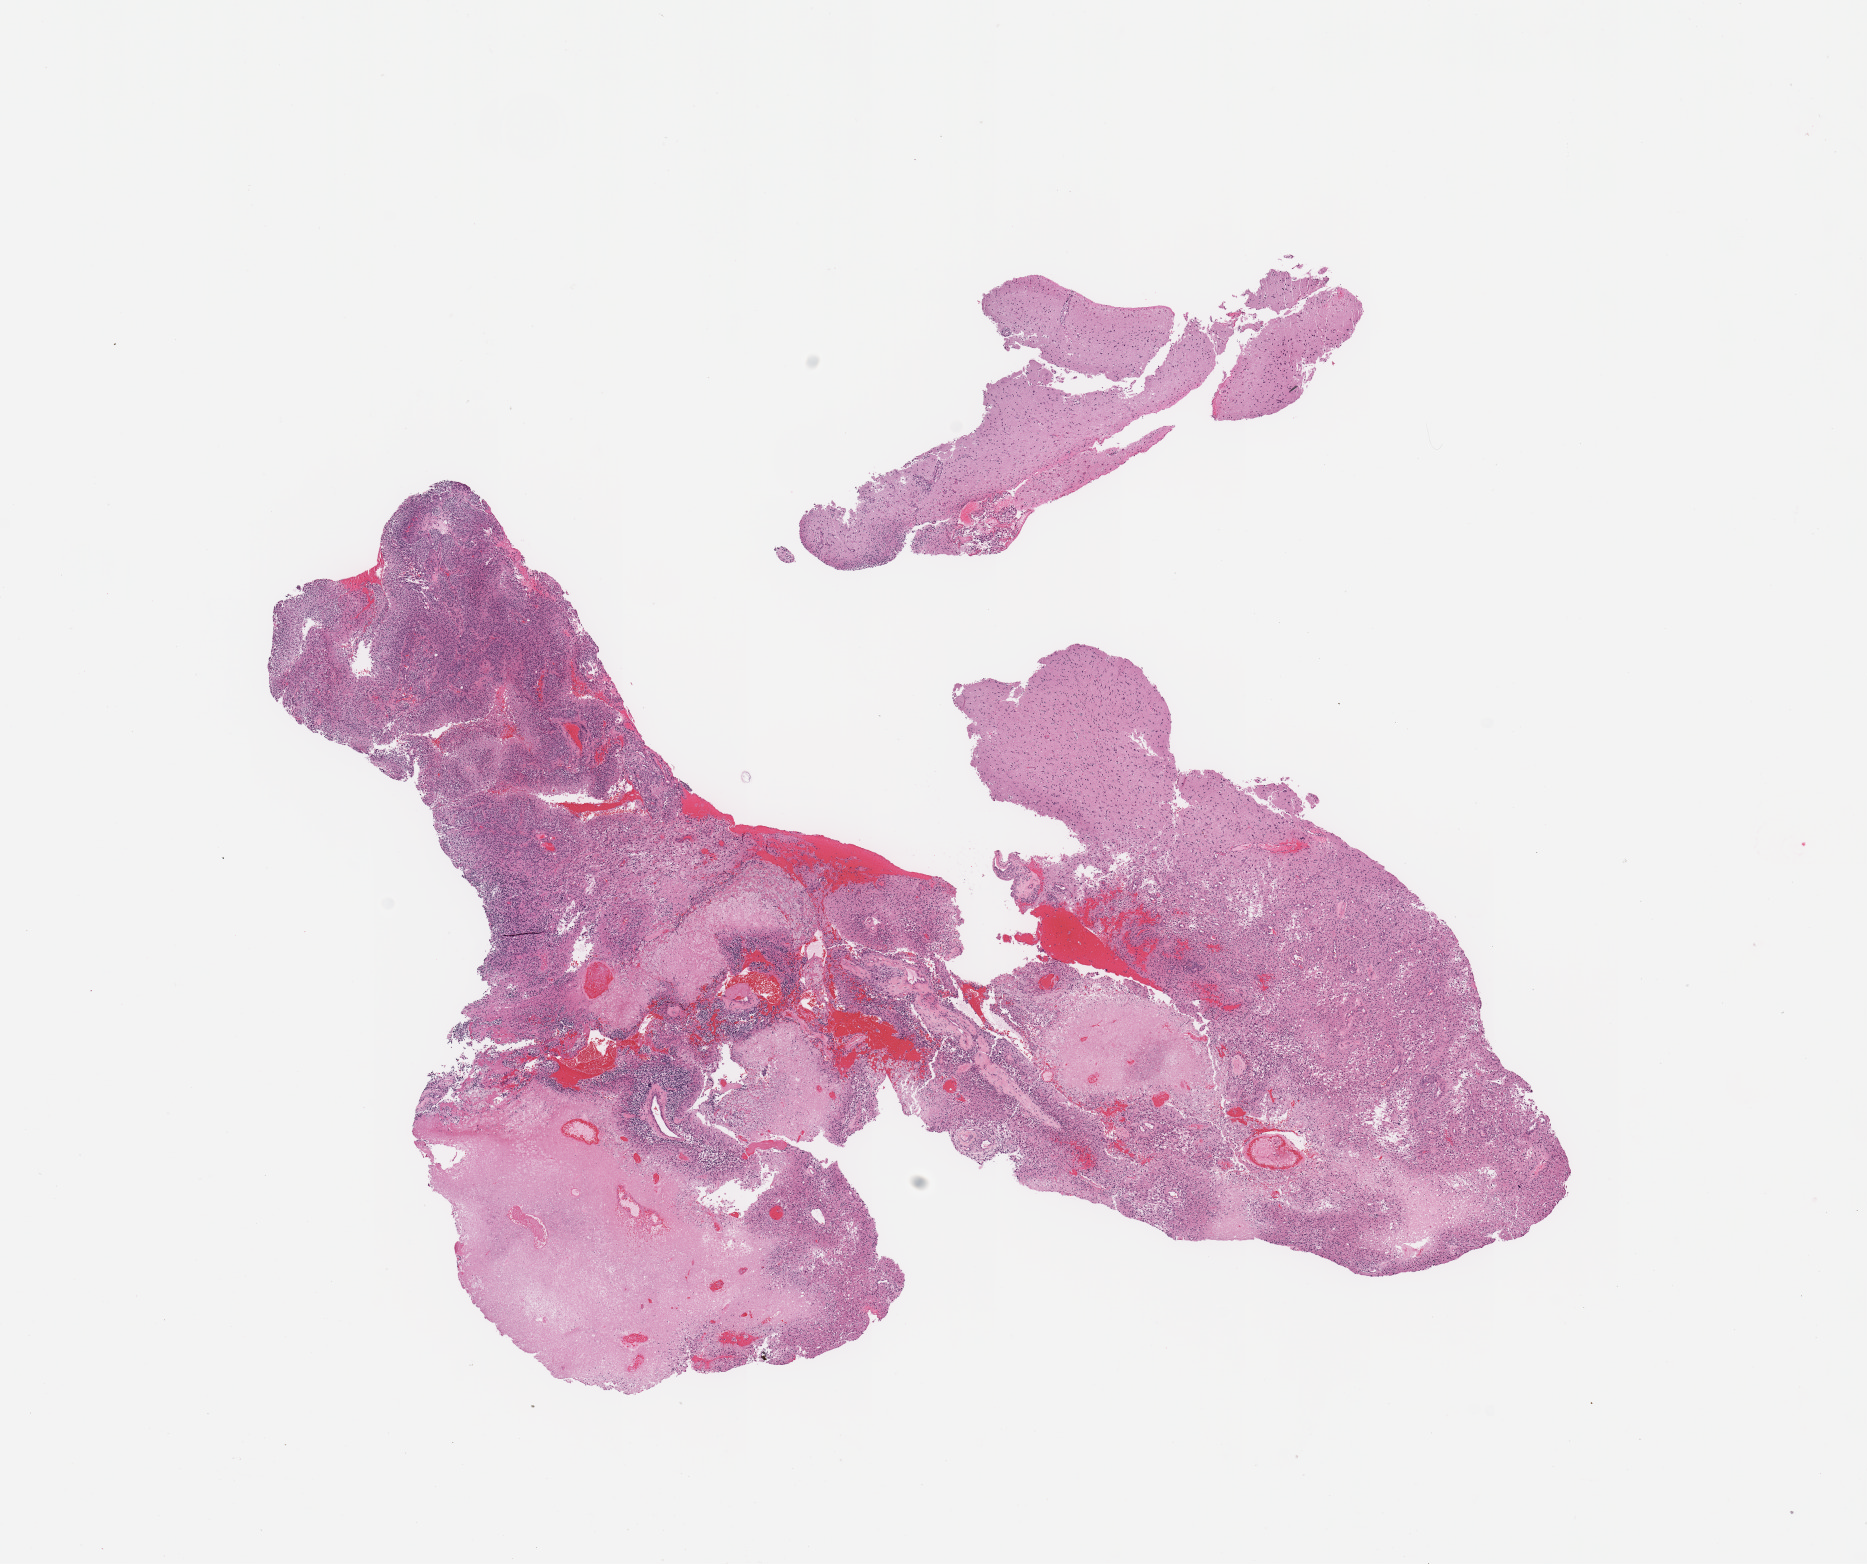
Hematoxylin and eosin (H&E) stained whole-slide image, shown as a low-resolution overview of the whole scanned area (about 14.8 x 12.4 mm). Tumour tissue sample, sampled site: brain. 72-year-old female patient. Pathologist review of this section (percent, as recorded): tumour nuclei 65%, necrosis 35%.
• primary tumour site (as recorded): temporal lobe
• histologic diagnosis: Glioblastoma